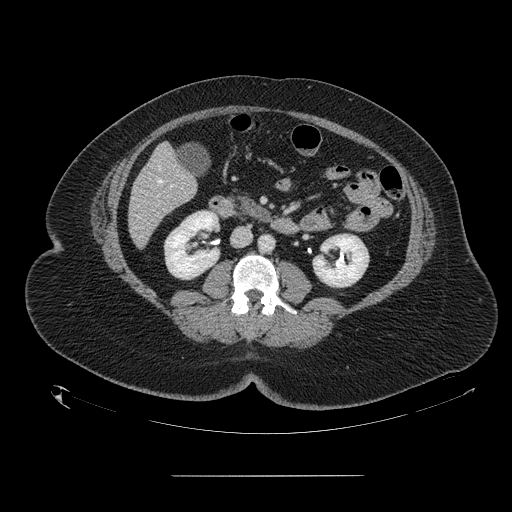
Contrast-enhanced abdominal CT, one axial slice; slice 48 of 164 in the series (ordered by position); 120 kVp; intravenous contrast given; soft-tissue window (W 400 / L 40 HU); 2.5 mm slice thickness; 512 × 512 image matrix, field of view 495 × 495 mm. Female patient, age 52 years. Case-level facts recorded for this patient, not image findings: diagnosis: colorectal cancer liver metastases, imaged before liver resection; multiple liver metastases: yes; largest metastasis: 3.5 cm; disease in both lobes: no.
Outlined on this slice (outlined manually by an expert reader):
- hepatic veins: bounding box [x1, y1, x2, y2] px = [158, 165, 162, 184]
- liver: [129, 145, 197, 246]
- portal vein (with intrahepatic branches): [157, 194, 159, 196]